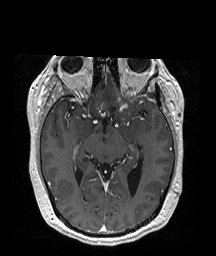
Brain MRI from a brain-tumour surgery series, one axial slice; position 109 of 192 along the scan axis; T1-weighted post-contrast; 1 mm slice thickness; 216 × 256 image matrix, field of view 211 × 250 mm. From the clinical record (not read from this slice): histopathology: Oligodendroglioma; WHO grade: 2; IDH mutation: yes; tumour location: Left Frontal (septal).
Outlined on this slice (manually delineated by an expert):
- tumour: bounding box [x1, y1, x2, y2] px = [107, 95, 132, 108]